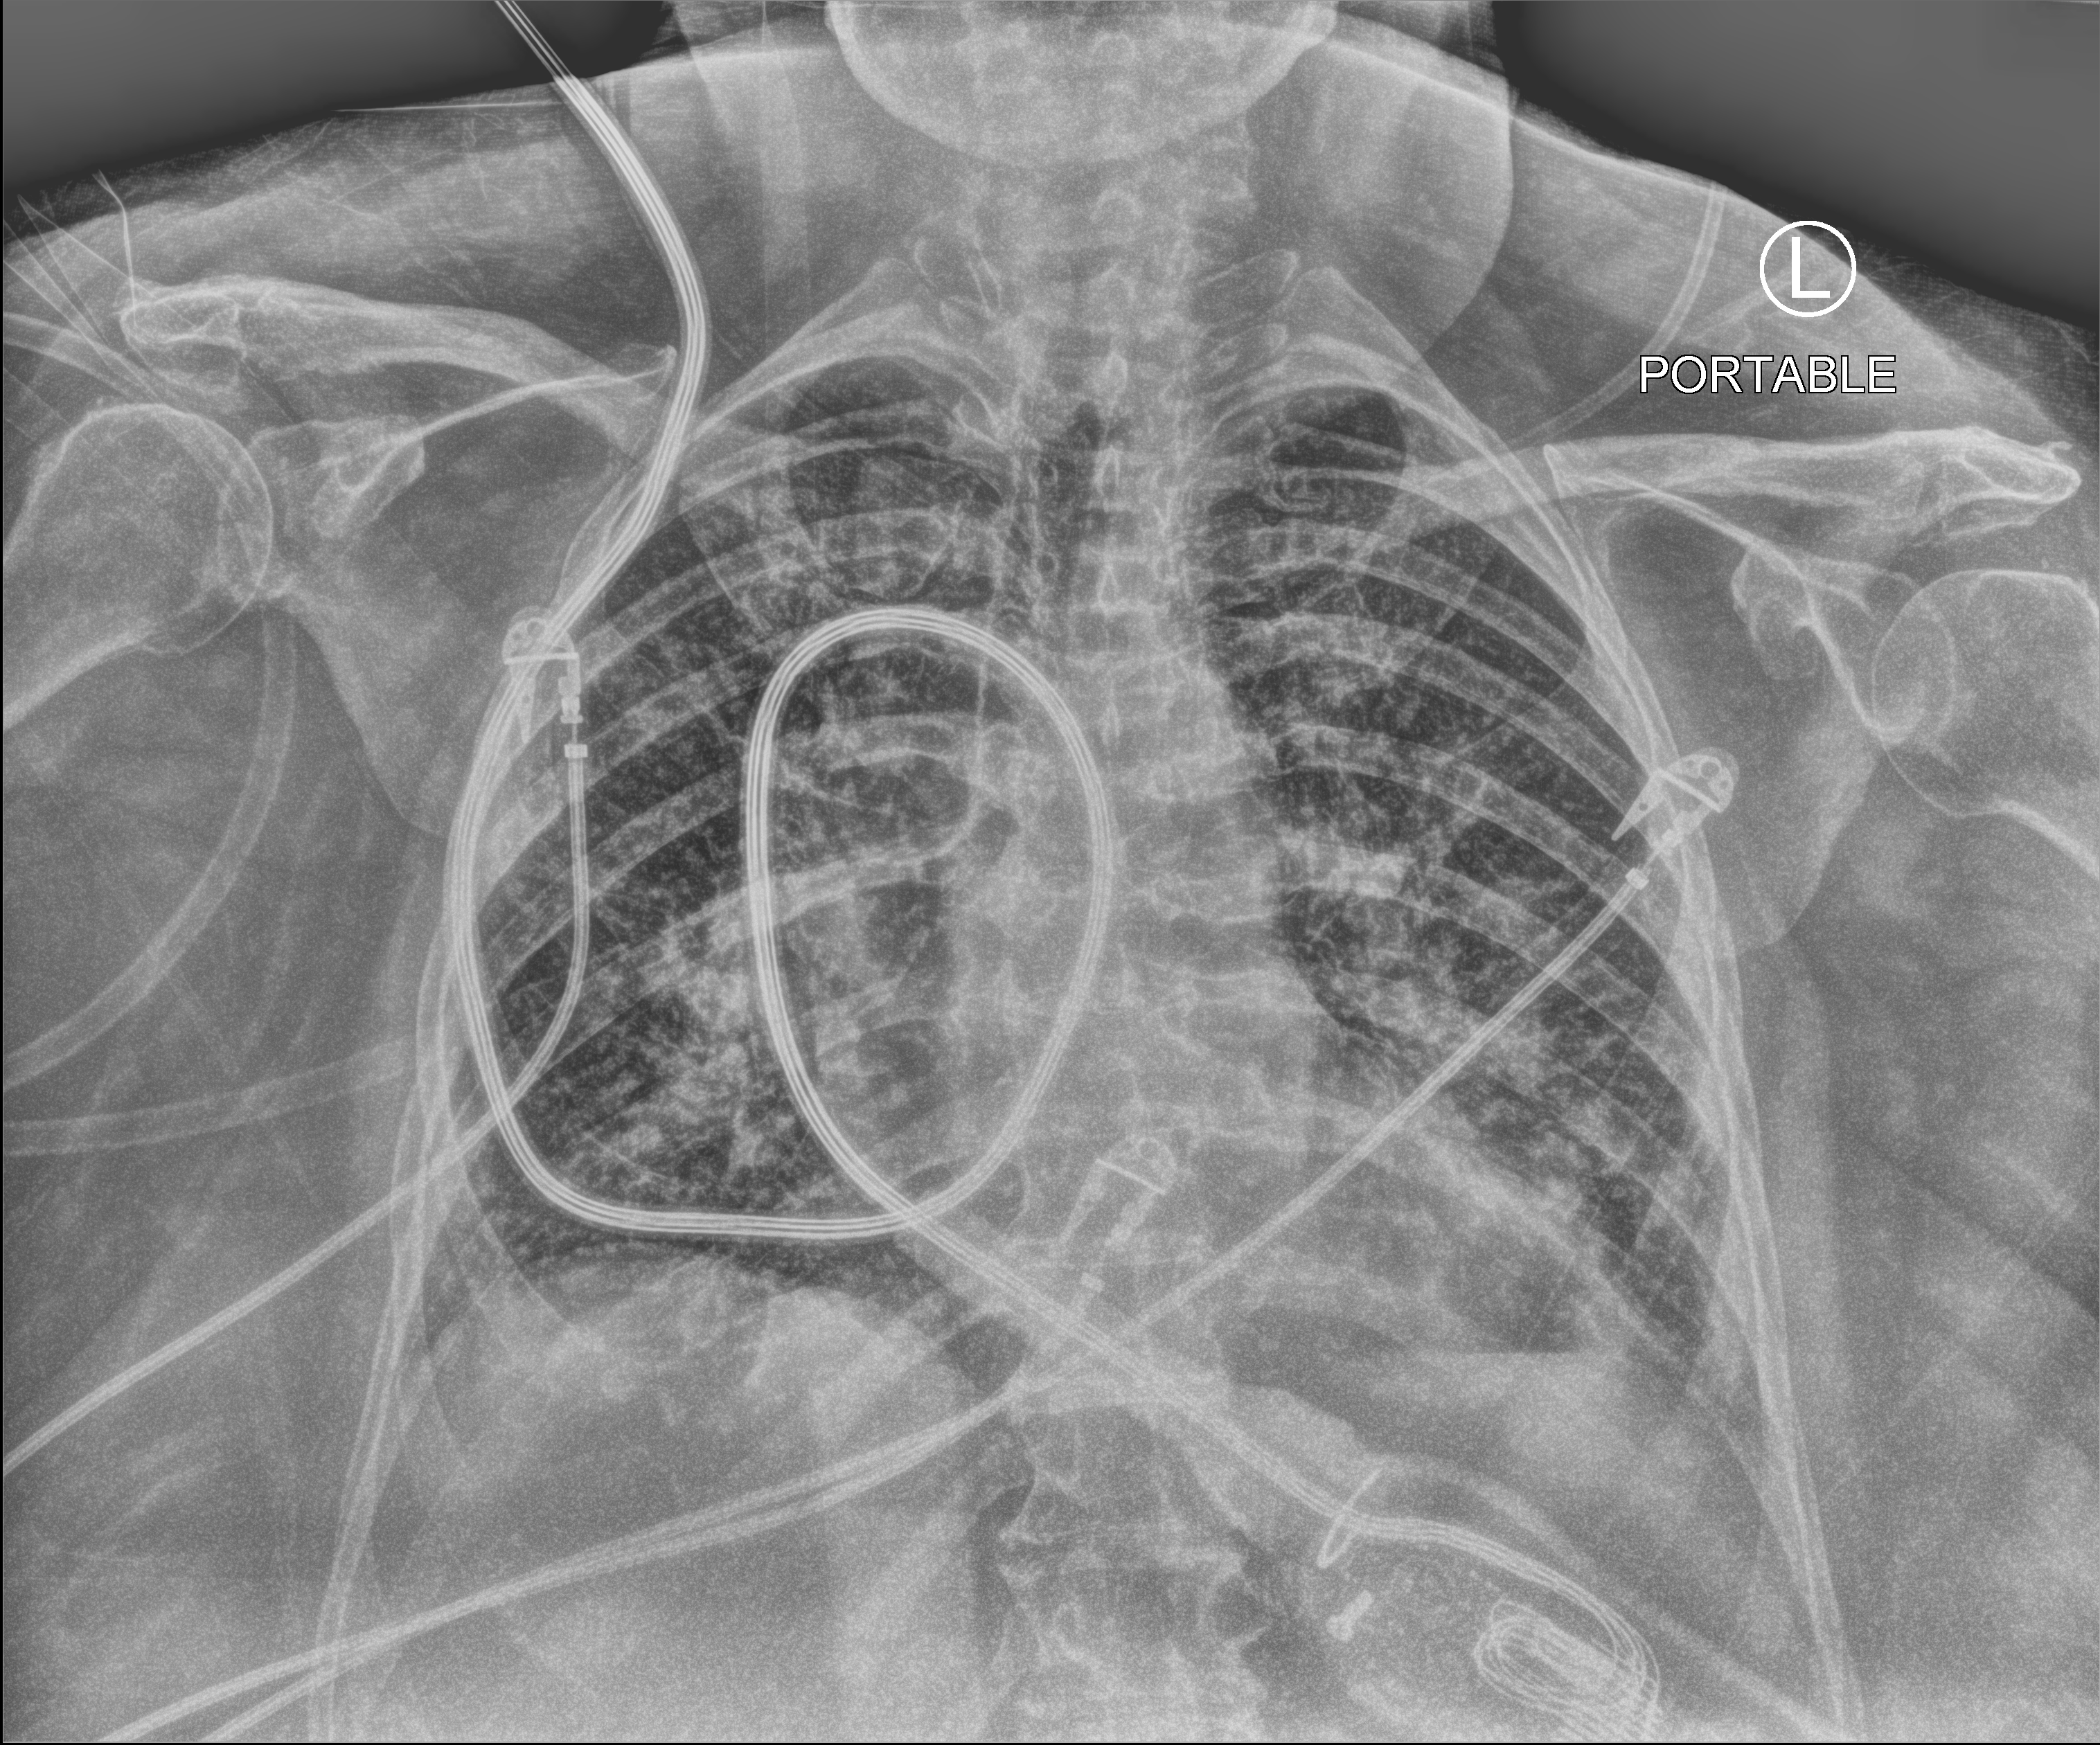
Portable chest radiograph; anteroposterior (AP) projection. Female patient hospitalised with COVID-19, age 75–90 years.
Admission-level facts for this patient (not findings on this image; timing relative to this image not recorded): length of hospital stay: 19 days; chronic kidney disease (admission record): no; admitted to intensive care during this hospital stay: no.